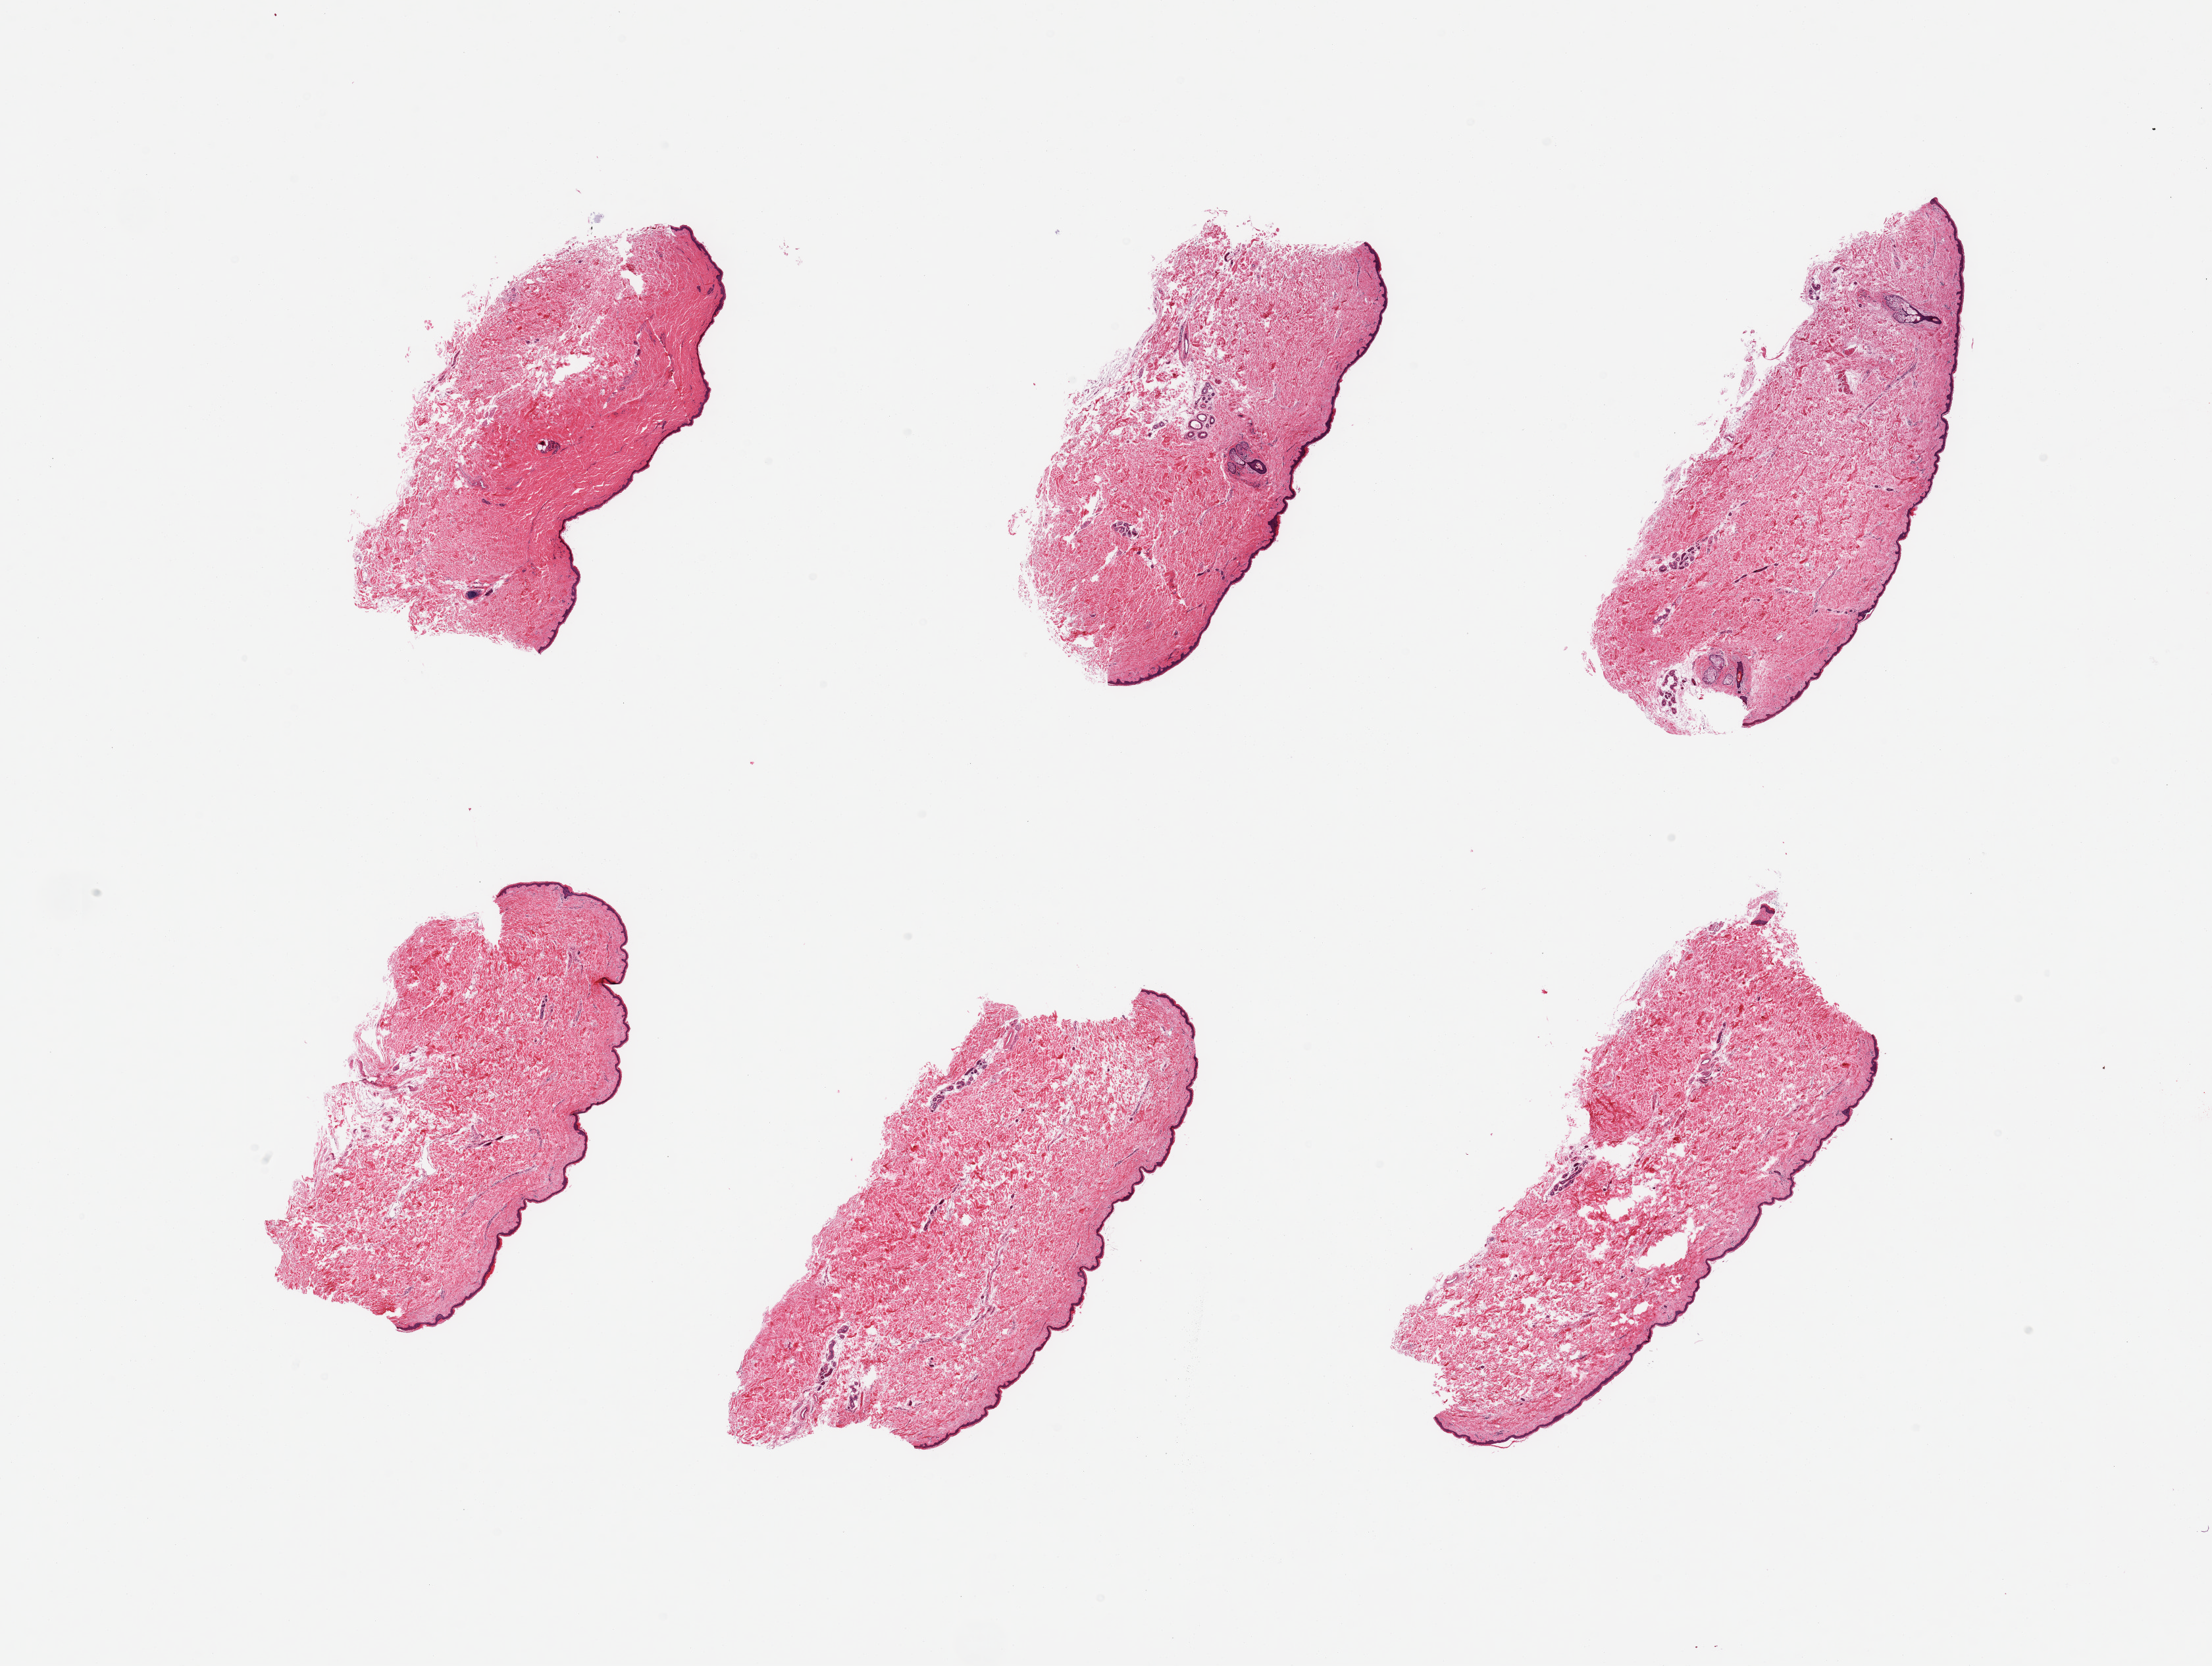
Whole-slide image, H&E stain, low-resolution overview of the scanned area, about 26.6 x 20.0 mm; PAXgene-fixed paraffin-embedded (PFPE) section; section of skin of suprapubic region (target tissue); donor tissue sample. Donor: female.
Pathologist's review note for this sample: 6 pieces, trace dermal fat; squamous epithelium is ~30-40 microns.